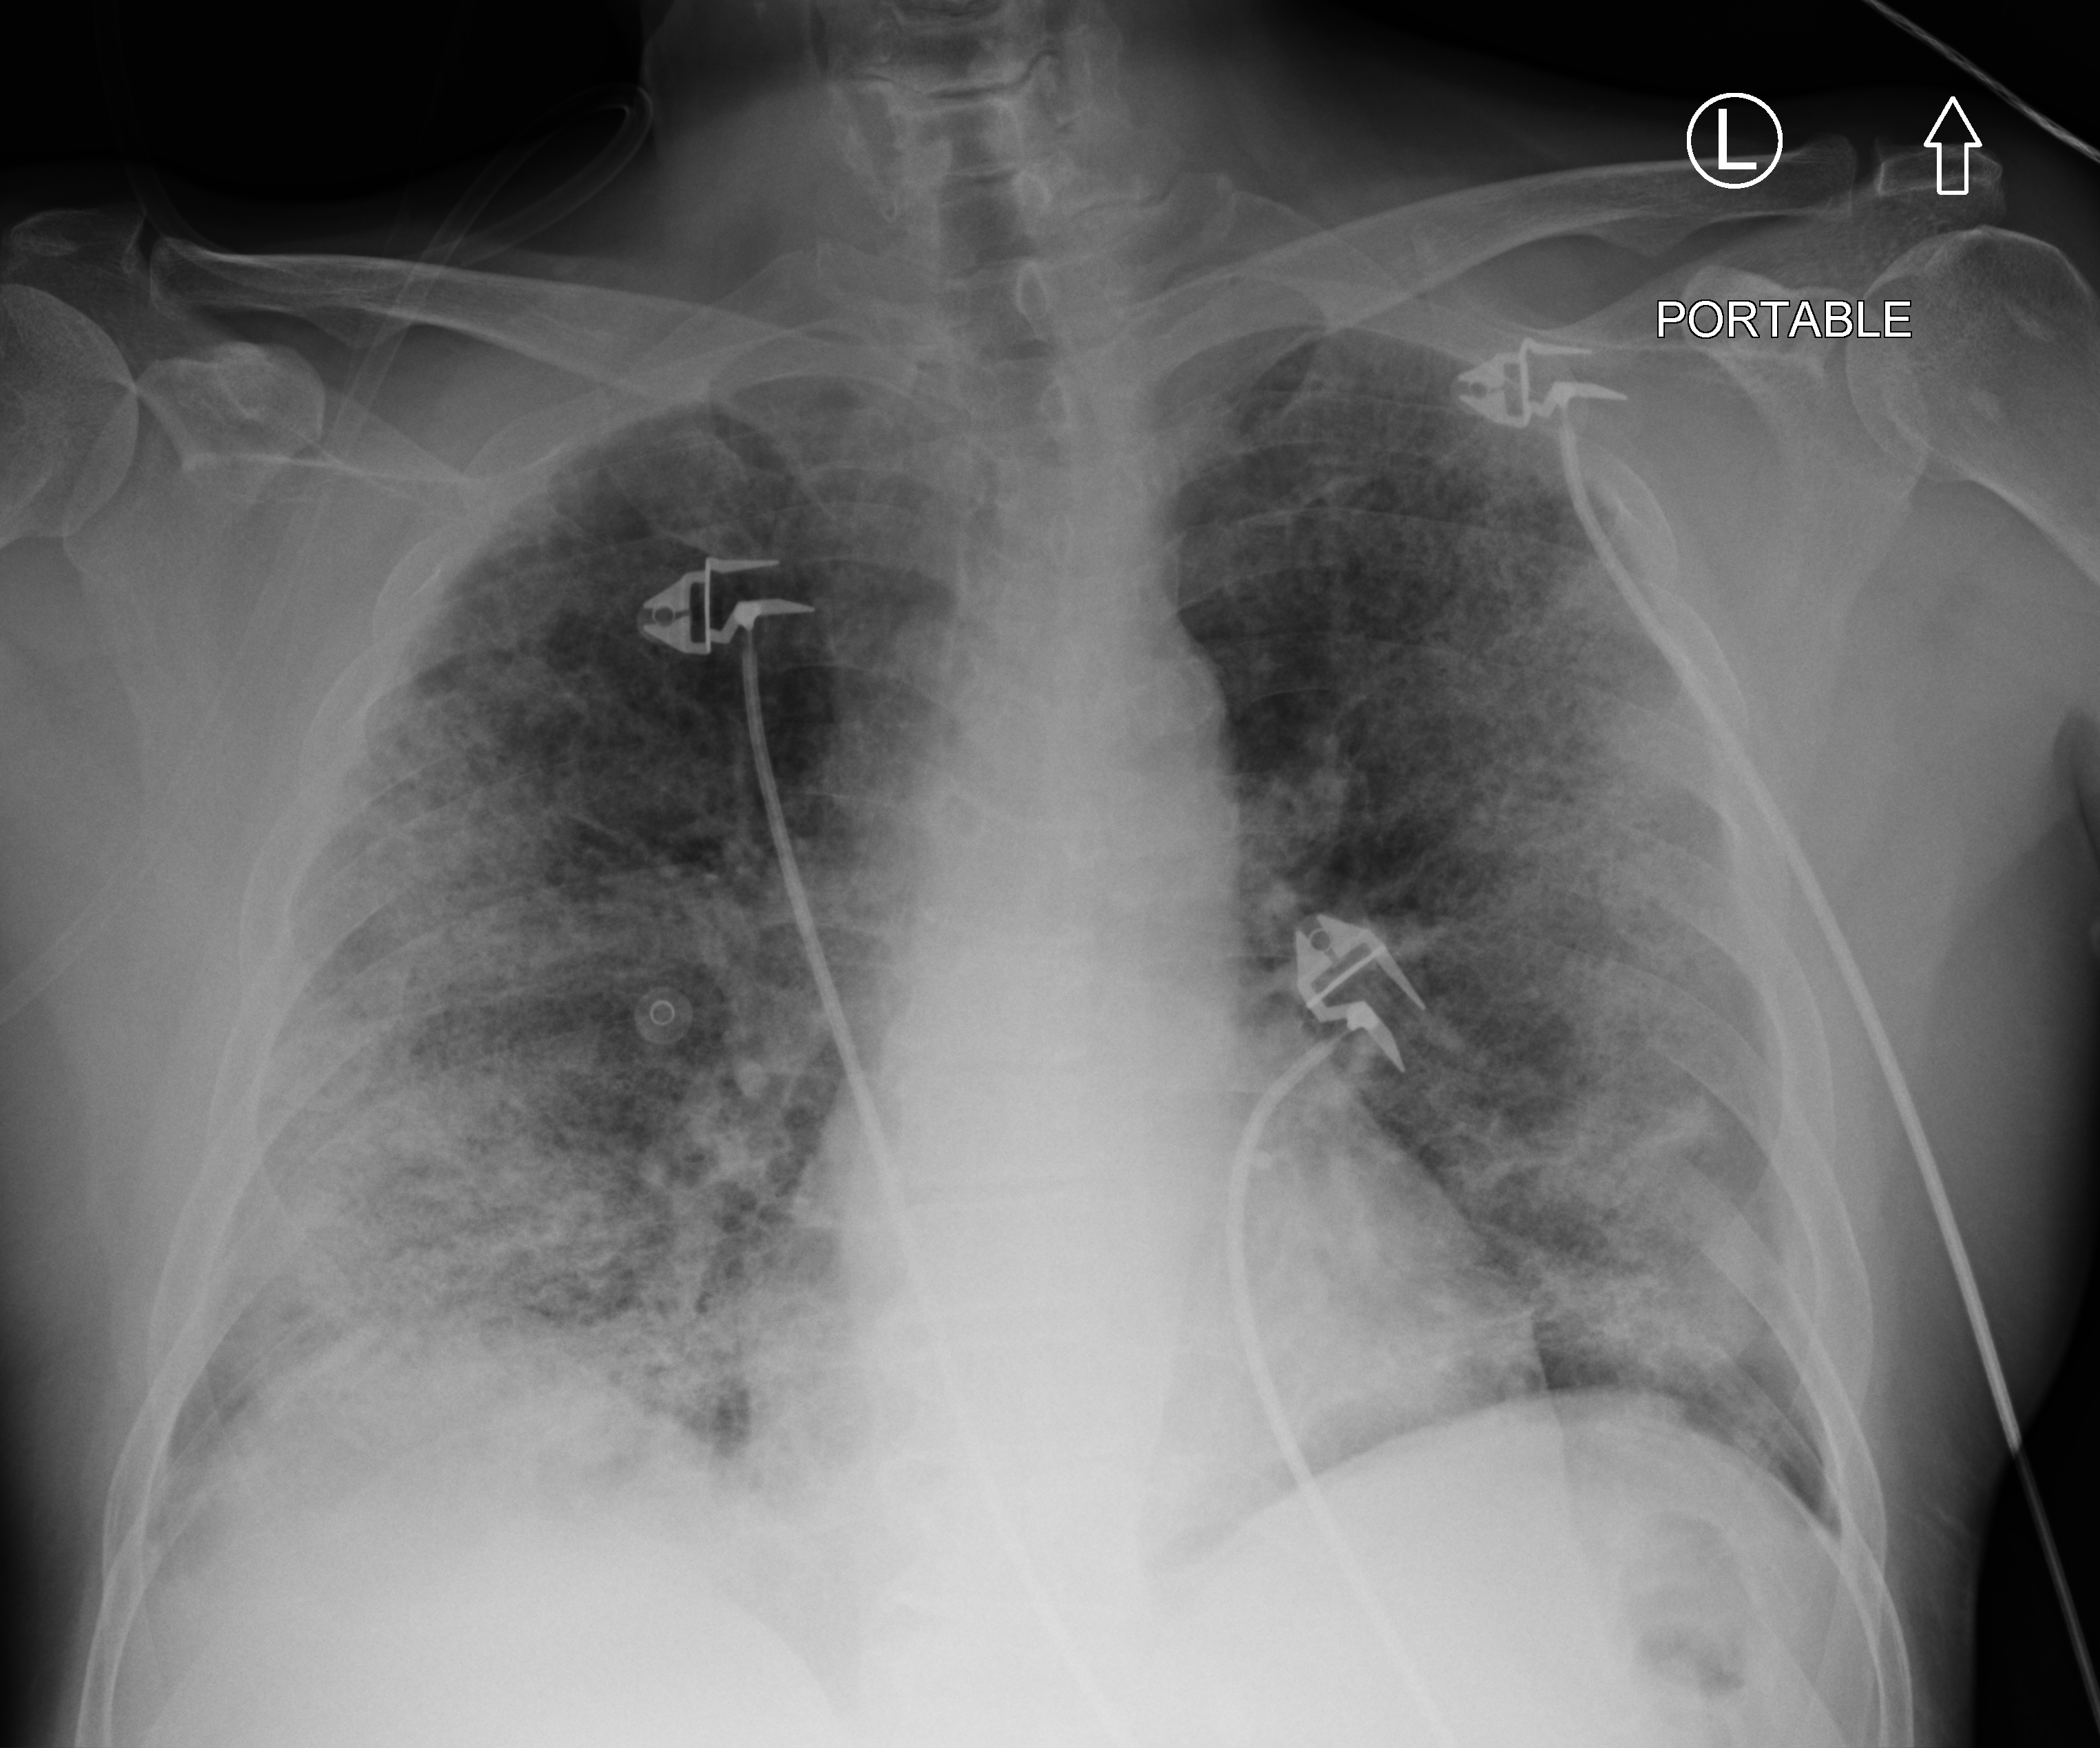
Chest X-ray (portable), anteroposterior (AP) projection. Male patient hospitalised with COVID-19, age 18–59 years.
From the hospital-stay record, not from the radiograph (when in the stay this image was taken is not recorded): admitted to intensive care during this hospital stay: no; mechanically ventilated during this hospital stay: no.